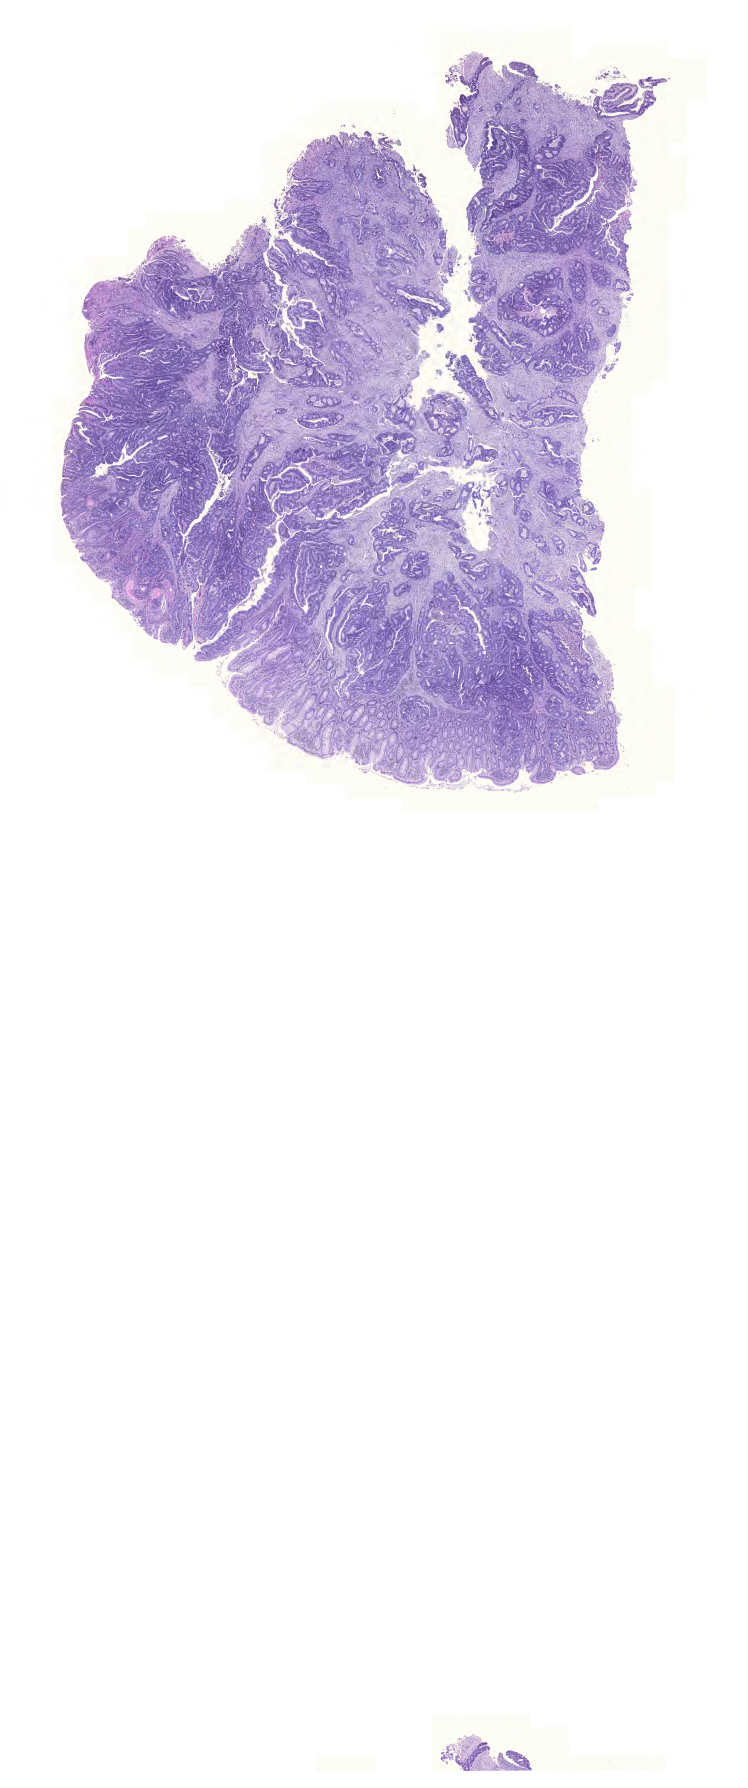
Digitized H&E-stained tissue section (whole slide), a low-resolution overview of the entire scanned area, about 11.1 x 26.6 mm (from a 20x scan); formalin-fixed paraffin-embedded (FFPE) diagnostic section; colon, primary tumour sample. Male patient; age at initial diagnosis 66 years.
AJCC pathologic stage: IIA. Pathologic diagnosis: Adenocarcinoma, NOS.